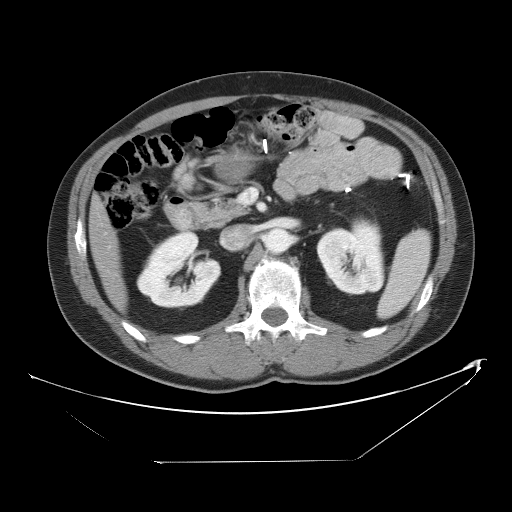
Contrast-enhanced abdominal CT, one axial slice; position 23 of 53 along the scan axis; 120 kVp; intravenous contrast given; soft-tissue window (W 400 / L 40 HU); 5 mm slice thickness; 512 × 512 image matrix. Male patient, age 59 years. From the clinical record (not read from this slice): diagnosis: colorectal cancer liver metastases, imaged before liver resection; multiple liver metastases: yes; largest metastasis: 8.5 cm; disease in both lobes: no.
Outlined on this slice (outlined manually by an expert reader):
- liver: bounding box (x1, y1, x2, y2) in pixels: (91, 201, 125, 308)
- planned liver remnant (the part of the liver to remain after resection): (90, 200, 125, 308)